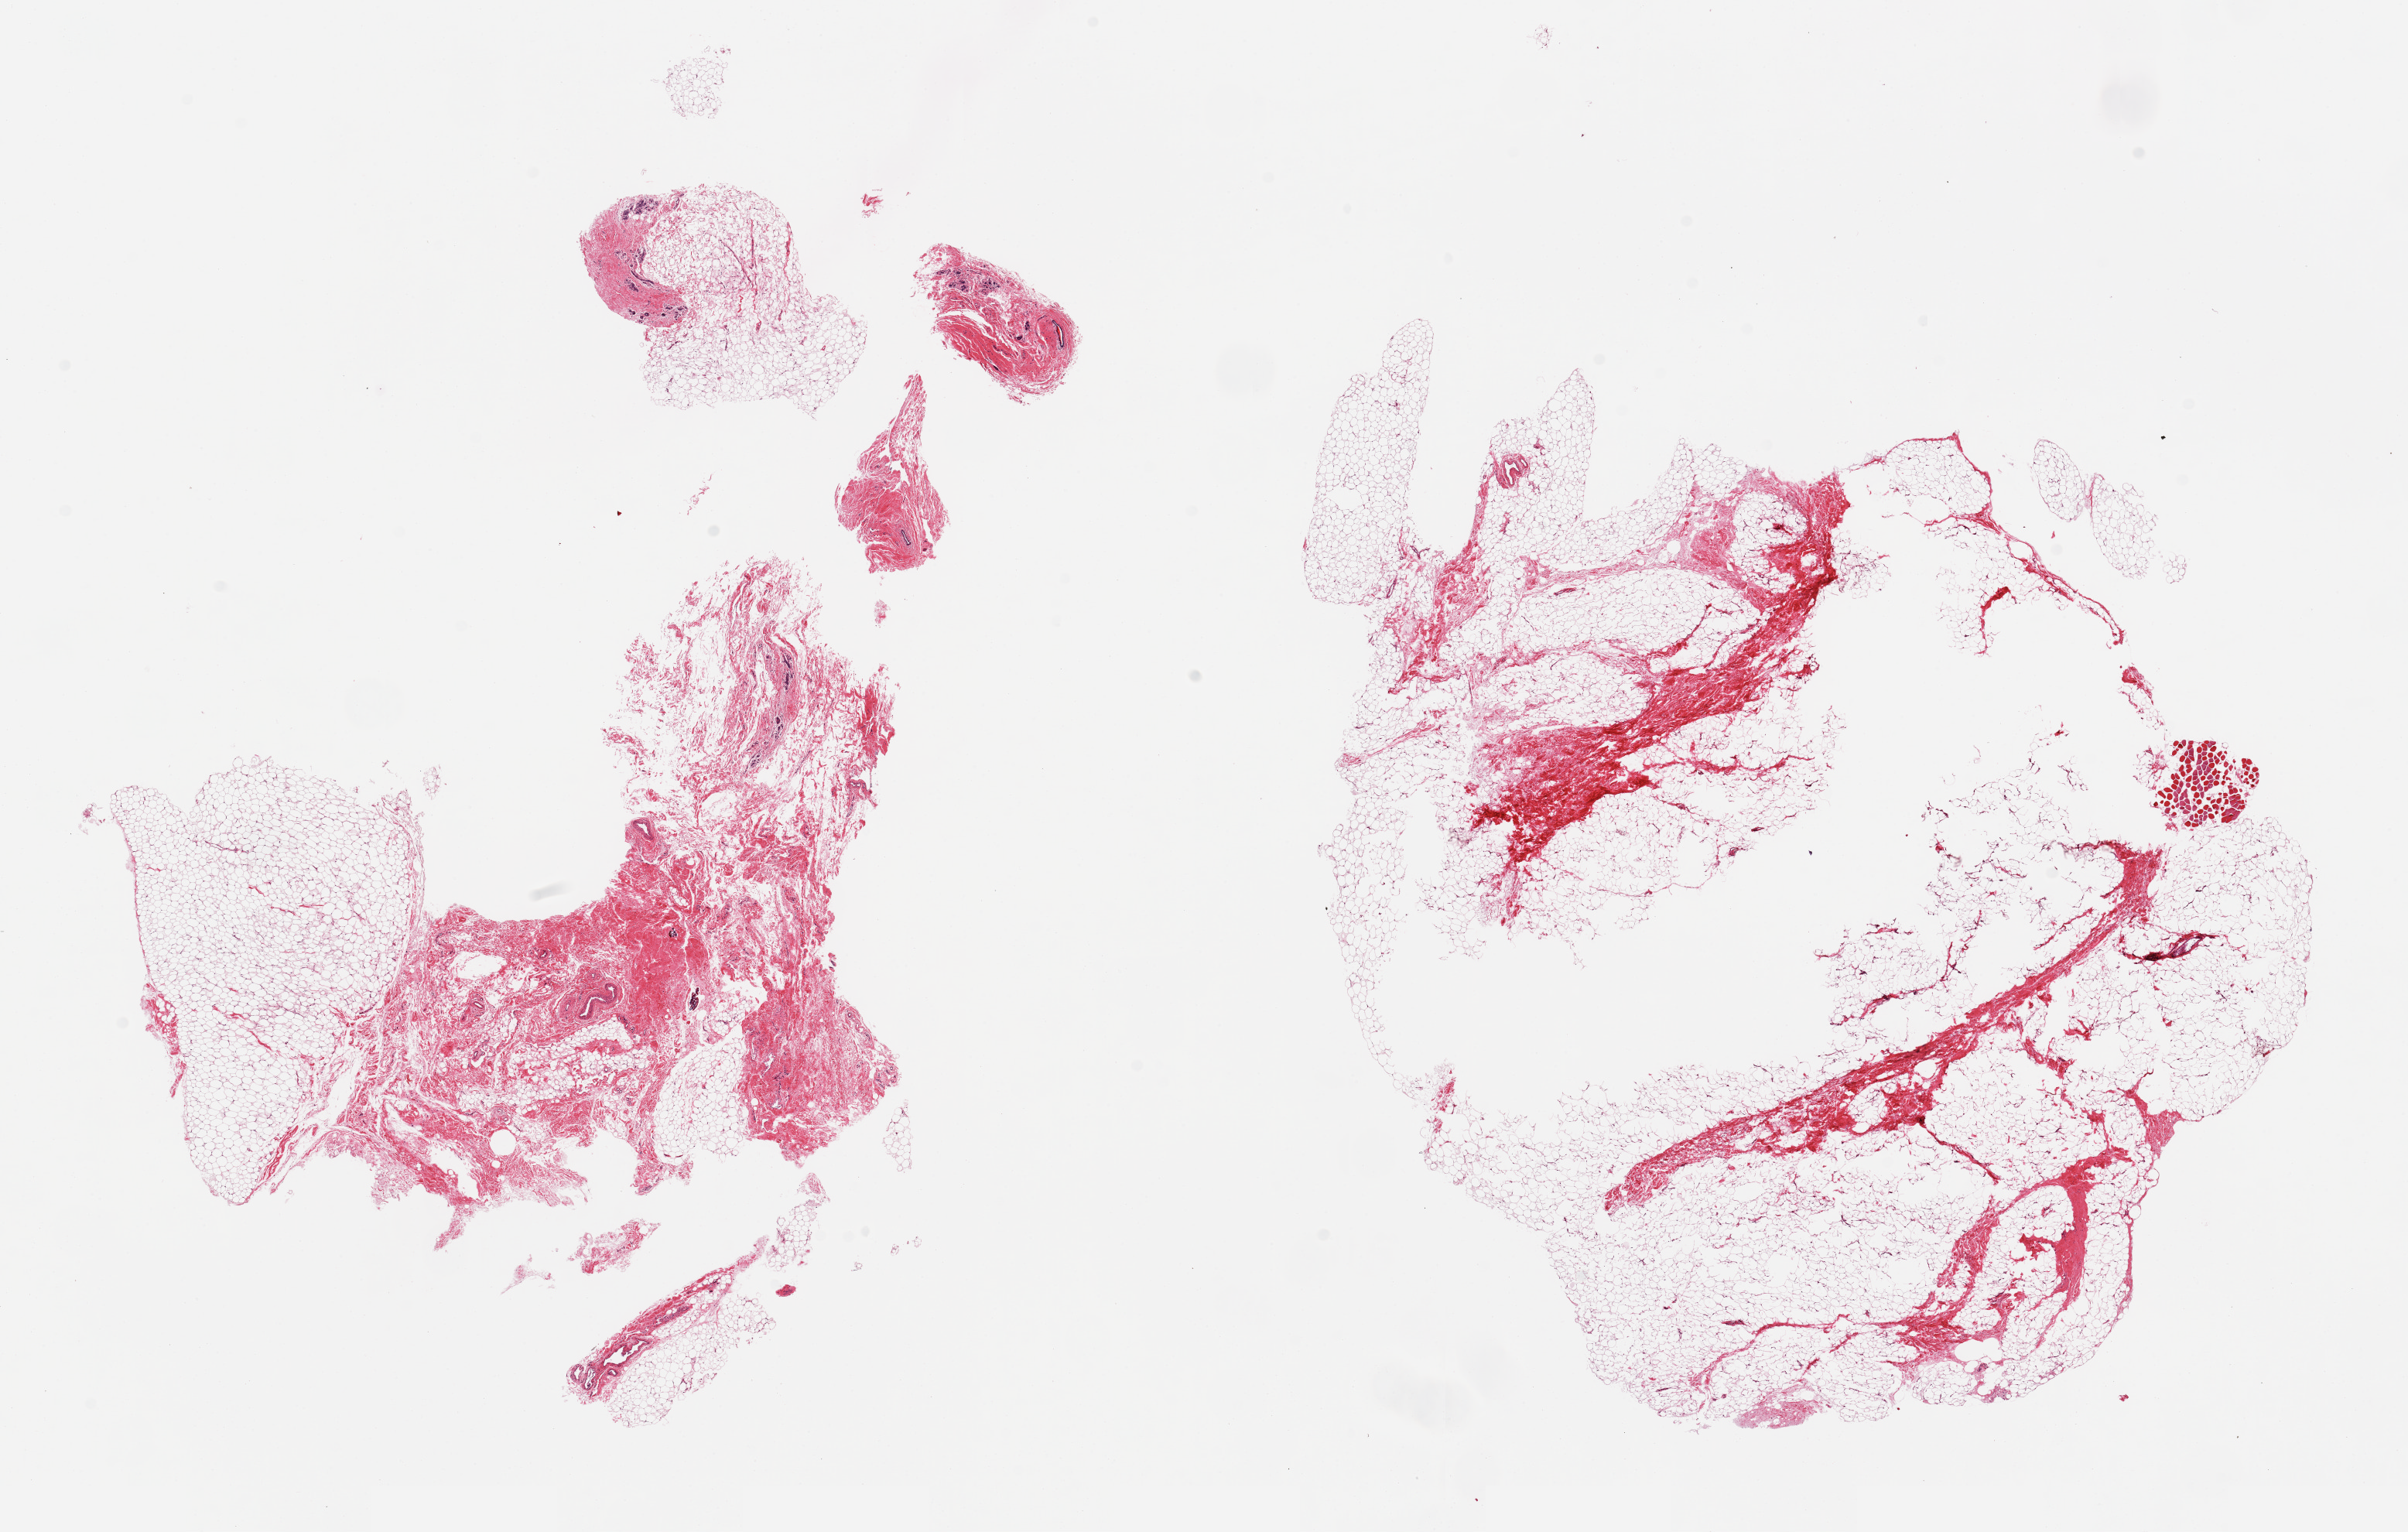
H&E whole-slide image — whole scanned area (about 24.6 x 15.7 mm, slide scanned at 20x) shown as a low-resolution overview, PAXgene-fixed, paraffin-embedded tissue, target tissue: breast, donor tissue sample. Donor sex: female.
- review note (as recorded): 2 pieces; central defect in one piece, fat and fibrous tissue with few ductal/lobular elements, small portion of skeletal muscle